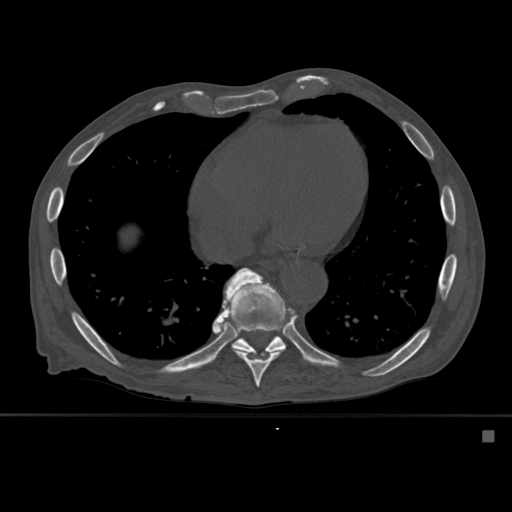
CT including the spine, one axial slice; slice 326 of 527 in the series (ordered by position); bone window (W 1800 / L 400 HU); 1.5 mm slice thickness; 512 × 512 image matrix. Patient: male, 78 years. Case-level facts recorded for this patient, not image findings: primary cancer: prostate.
Structures marked on this image (semi-automatic segmentation, software-assisted and operator-edited):
- T10 vertebra: bounding box [x1, y1, x2, y2] px = [231, 332, 286, 355]
- T9 vertebra: [218, 268, 297, 388]